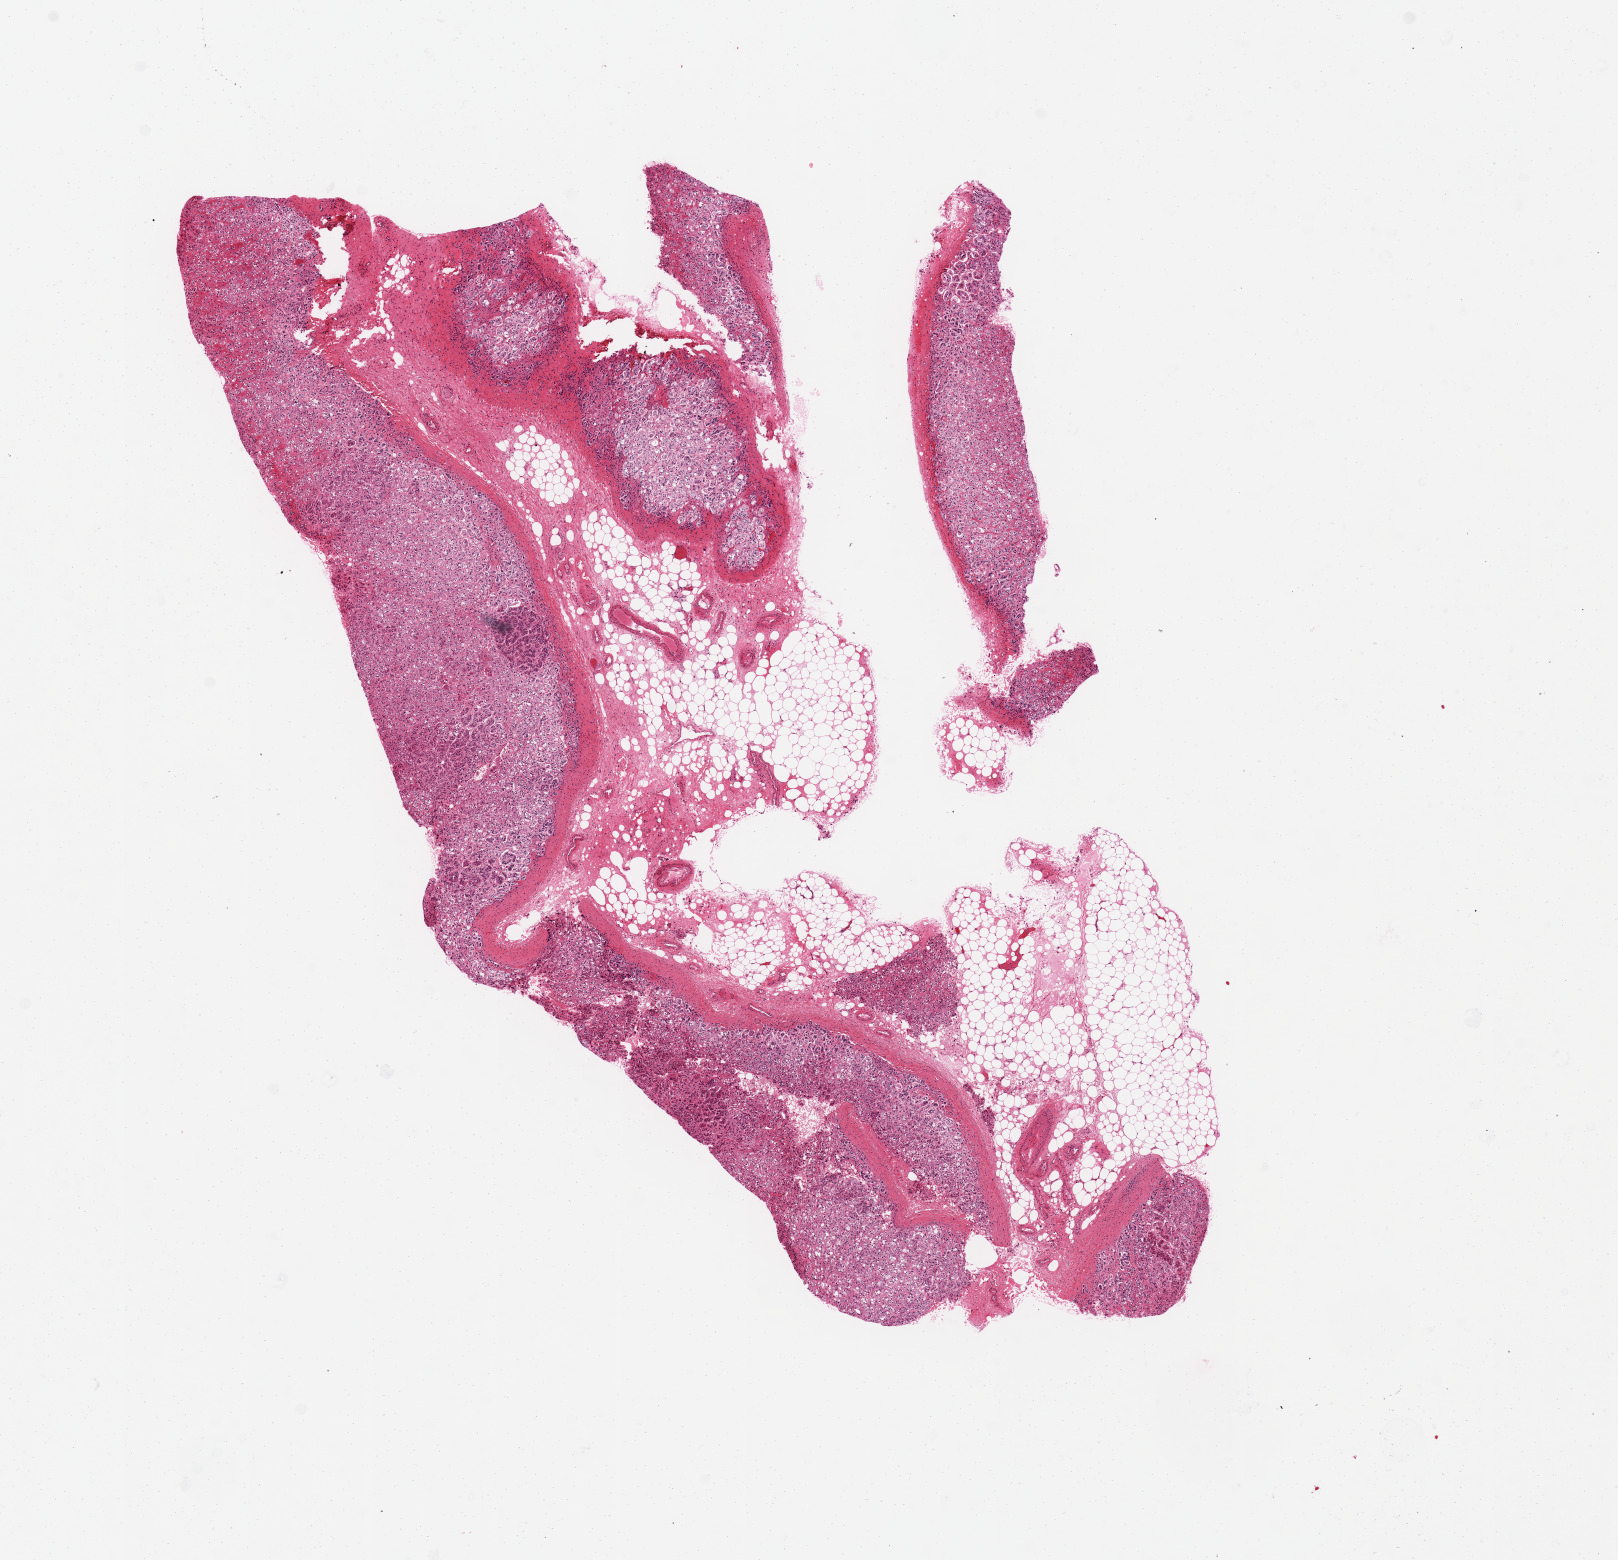
Whole-slide image, hematoxylin and eosin (H&E) stain — a low-resolution overview of the entire scanned area, about 12.8 x 12.3 mm, PAXgene-fixed paraffin-embedded (PFPE) section, section of adrenal gland (target tissue), tissue donor sample.
Pathologist's review note for this sample: 30% adipose tissue; remarkably well-preserved cortex; no medulla.